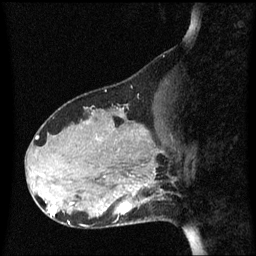
Breast MRI (dynamic contrast-enhanced), one sagittal slice; position 20 of 60 along the scan axis; dynamic contrast-enhanced series, image 2 of 3 at this slice position (ordered by acquisition); 1.5 T; TE 4.2 ms, TR 8.4 ms; 2.1 mm slice thickness; 256 × 256 image matrix, field of view 210 × 210 mm. Patient: female, 31 years. Case-level facts recorded for this patient, not image findings: setting: breast cancer imaged before/during neoadjuvant chemotherapy; receptor status: HR-positive, HER2-negative.
Outlined on this slice (semi-automatically segmented with operator editing):
- analysis volume of interest (the breast-tissue region the enhancement analysis was run in; not a lesion): bounding box [x1, y1, x2, y2] px = [98, 175, 165, 228]
- tumour enhancement mask (voxels above the 70 % enhancement threshold inside the analysis volume of interest): [121, 204, 132, 214]